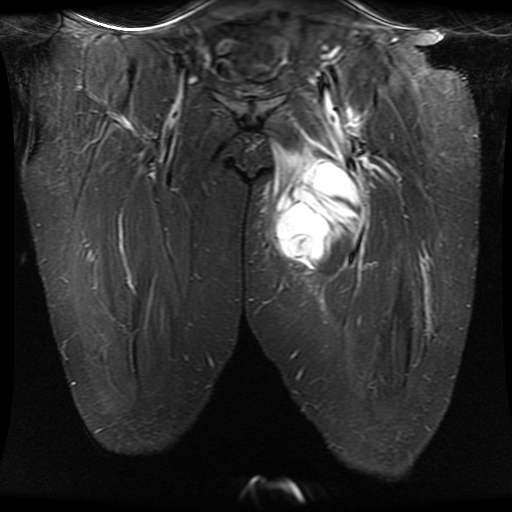
MRI of an extremity soft-tissue mass, one coronal slice. Slice 8 of 30 in the series (ordered by position). STIR. 512 × 512 image matrix, field of view 460 × 460 mm. Female patient. Case-level facts recorded for this patient, not image findings: histological type: myxofibrosarcoma; grade: intermediate; site of the primary tumour: left thigh.
Structures marked on this image (expert manual segmentation):
- gross tumour volume including surrounding oedema: bounding box (x1, y1, x2, y2) in pixels: (266, 90, 382, 273)
- gross tumour volume (mass): (275, 158, 363, 273)